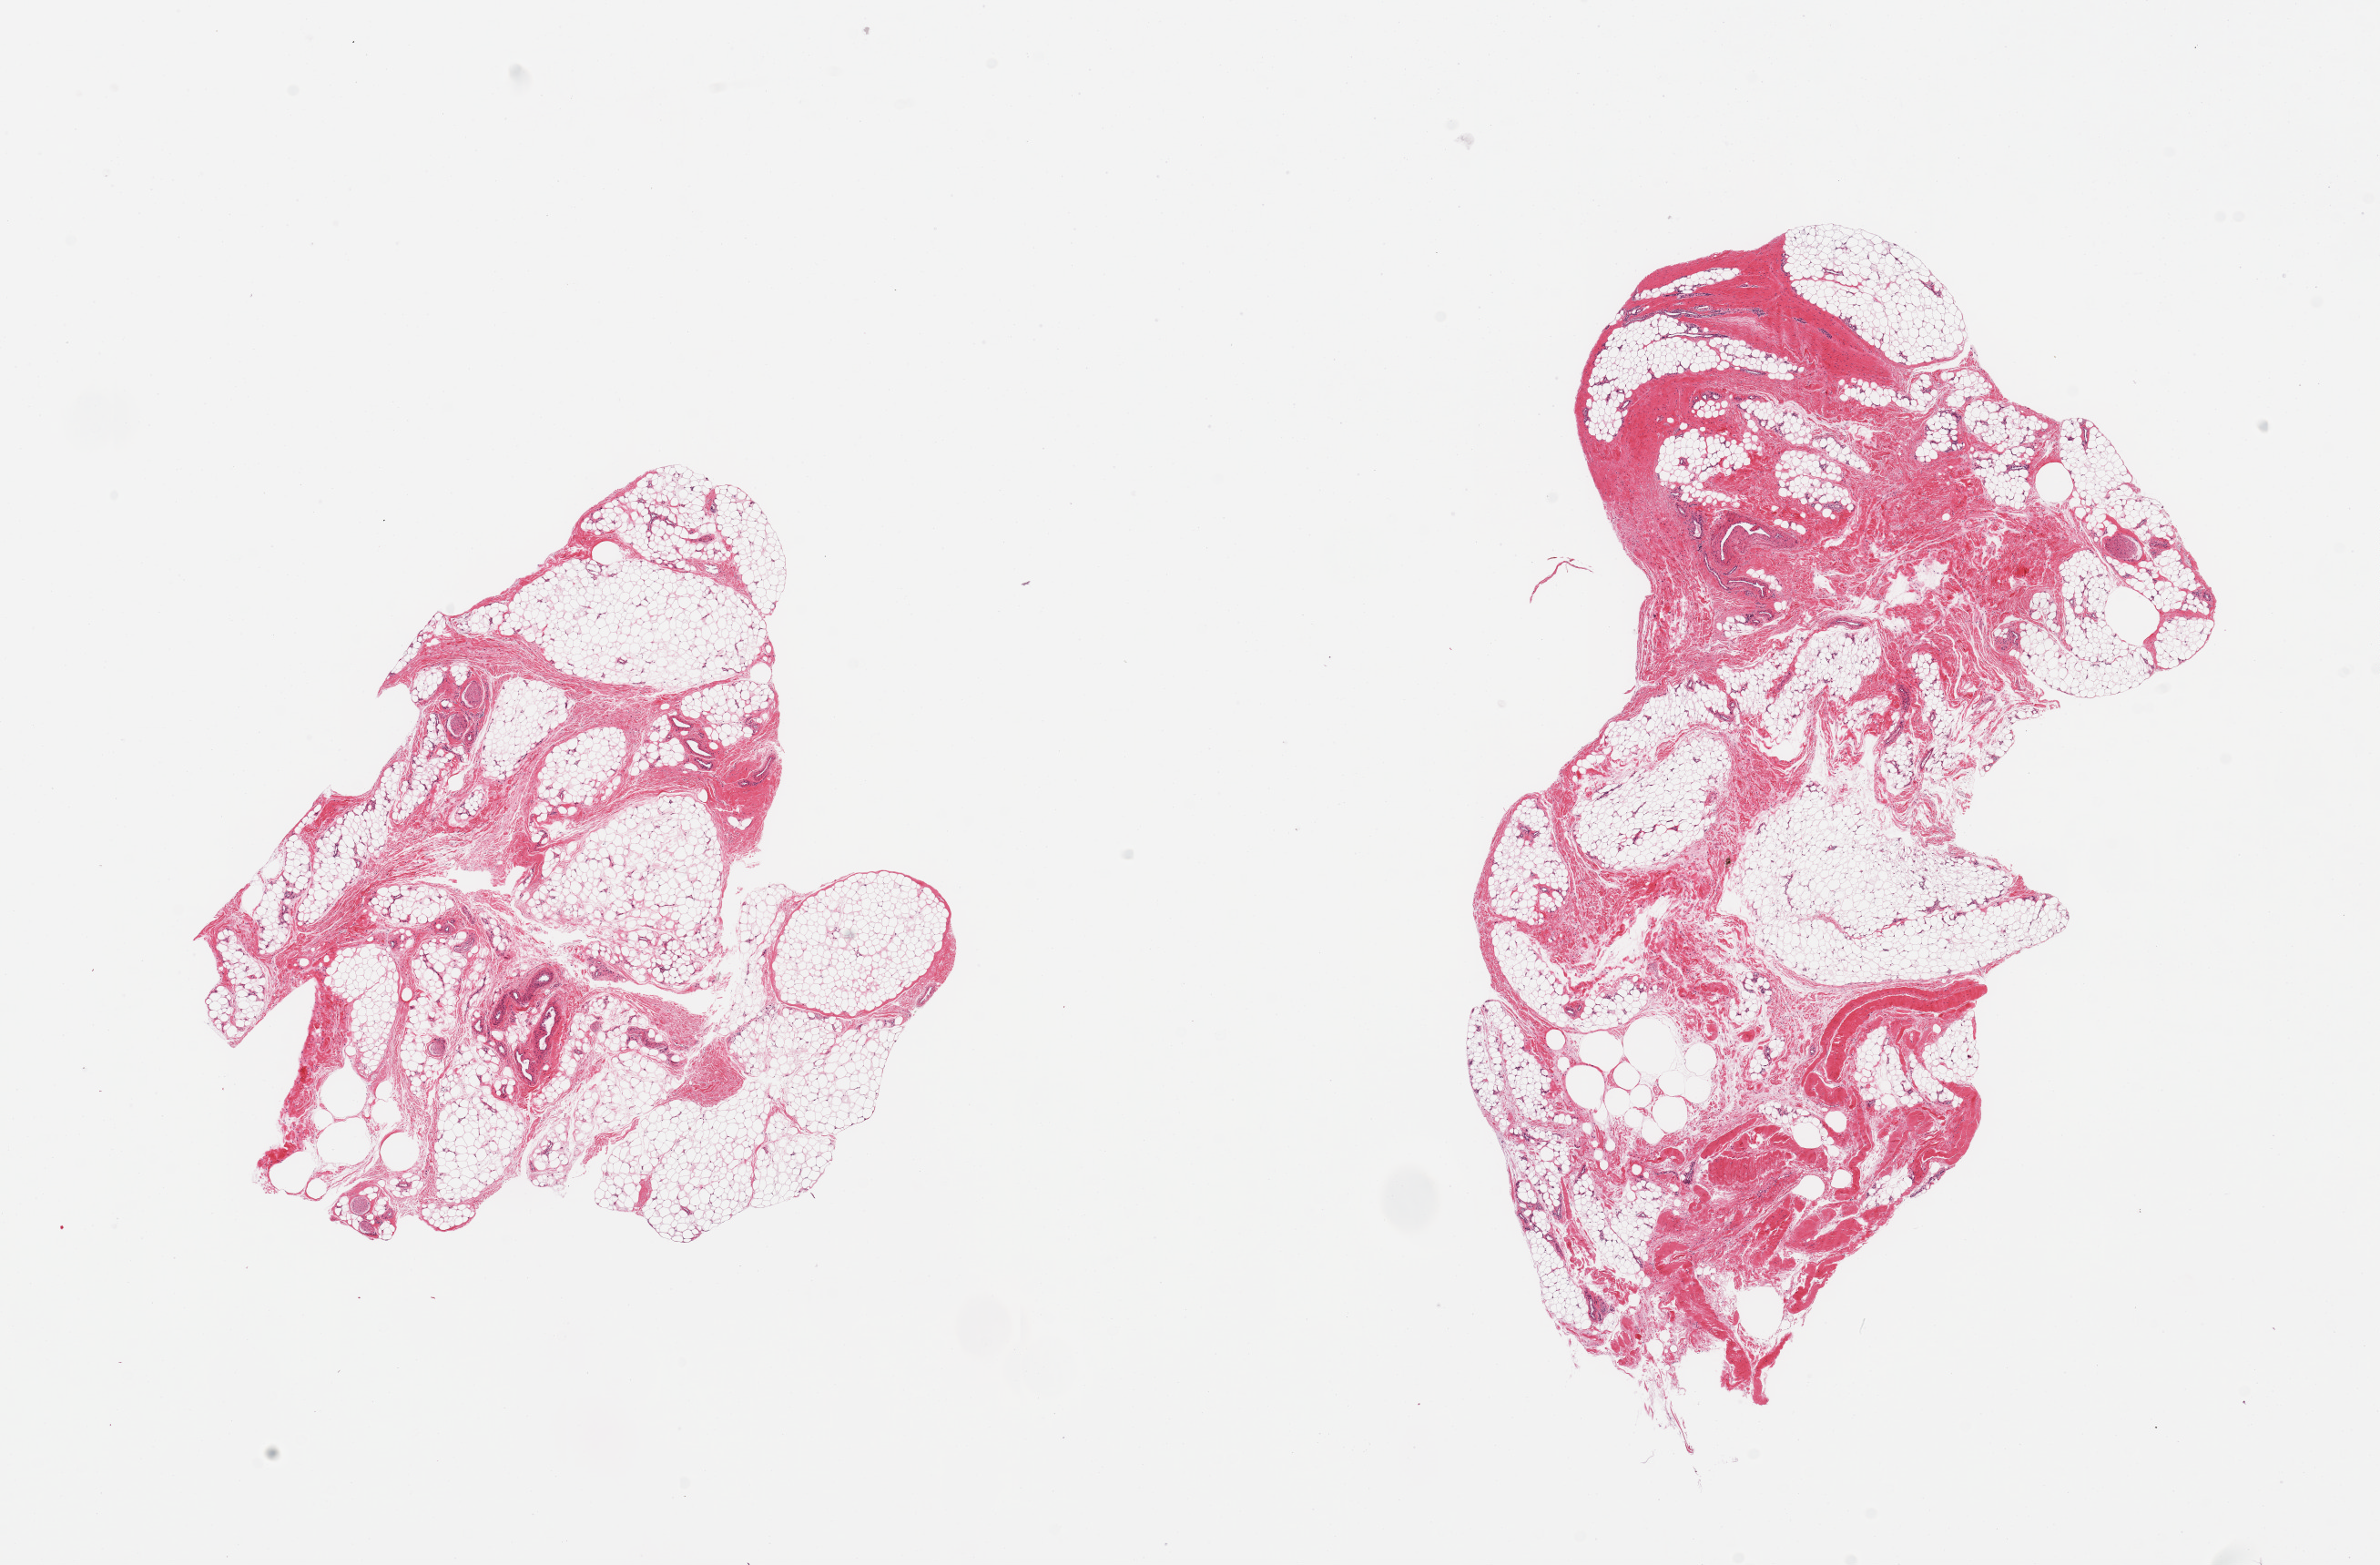
Haematoxylin and eosin whole-slide image — whole scanned area (about 20.7 x 13.6 mm, acquisition: 20x scan) shown as a low-resolution overview. PAXgene-fixed paraffin-embedded (PFPE) section. Sampled site (target tissue): adipose tissue. Donor tissue sample. Donor sex: male.
Review note (as recorded): 2 pieces; 80 and 60% fat, remainder is fibrous/nerve/vessel/tendon.